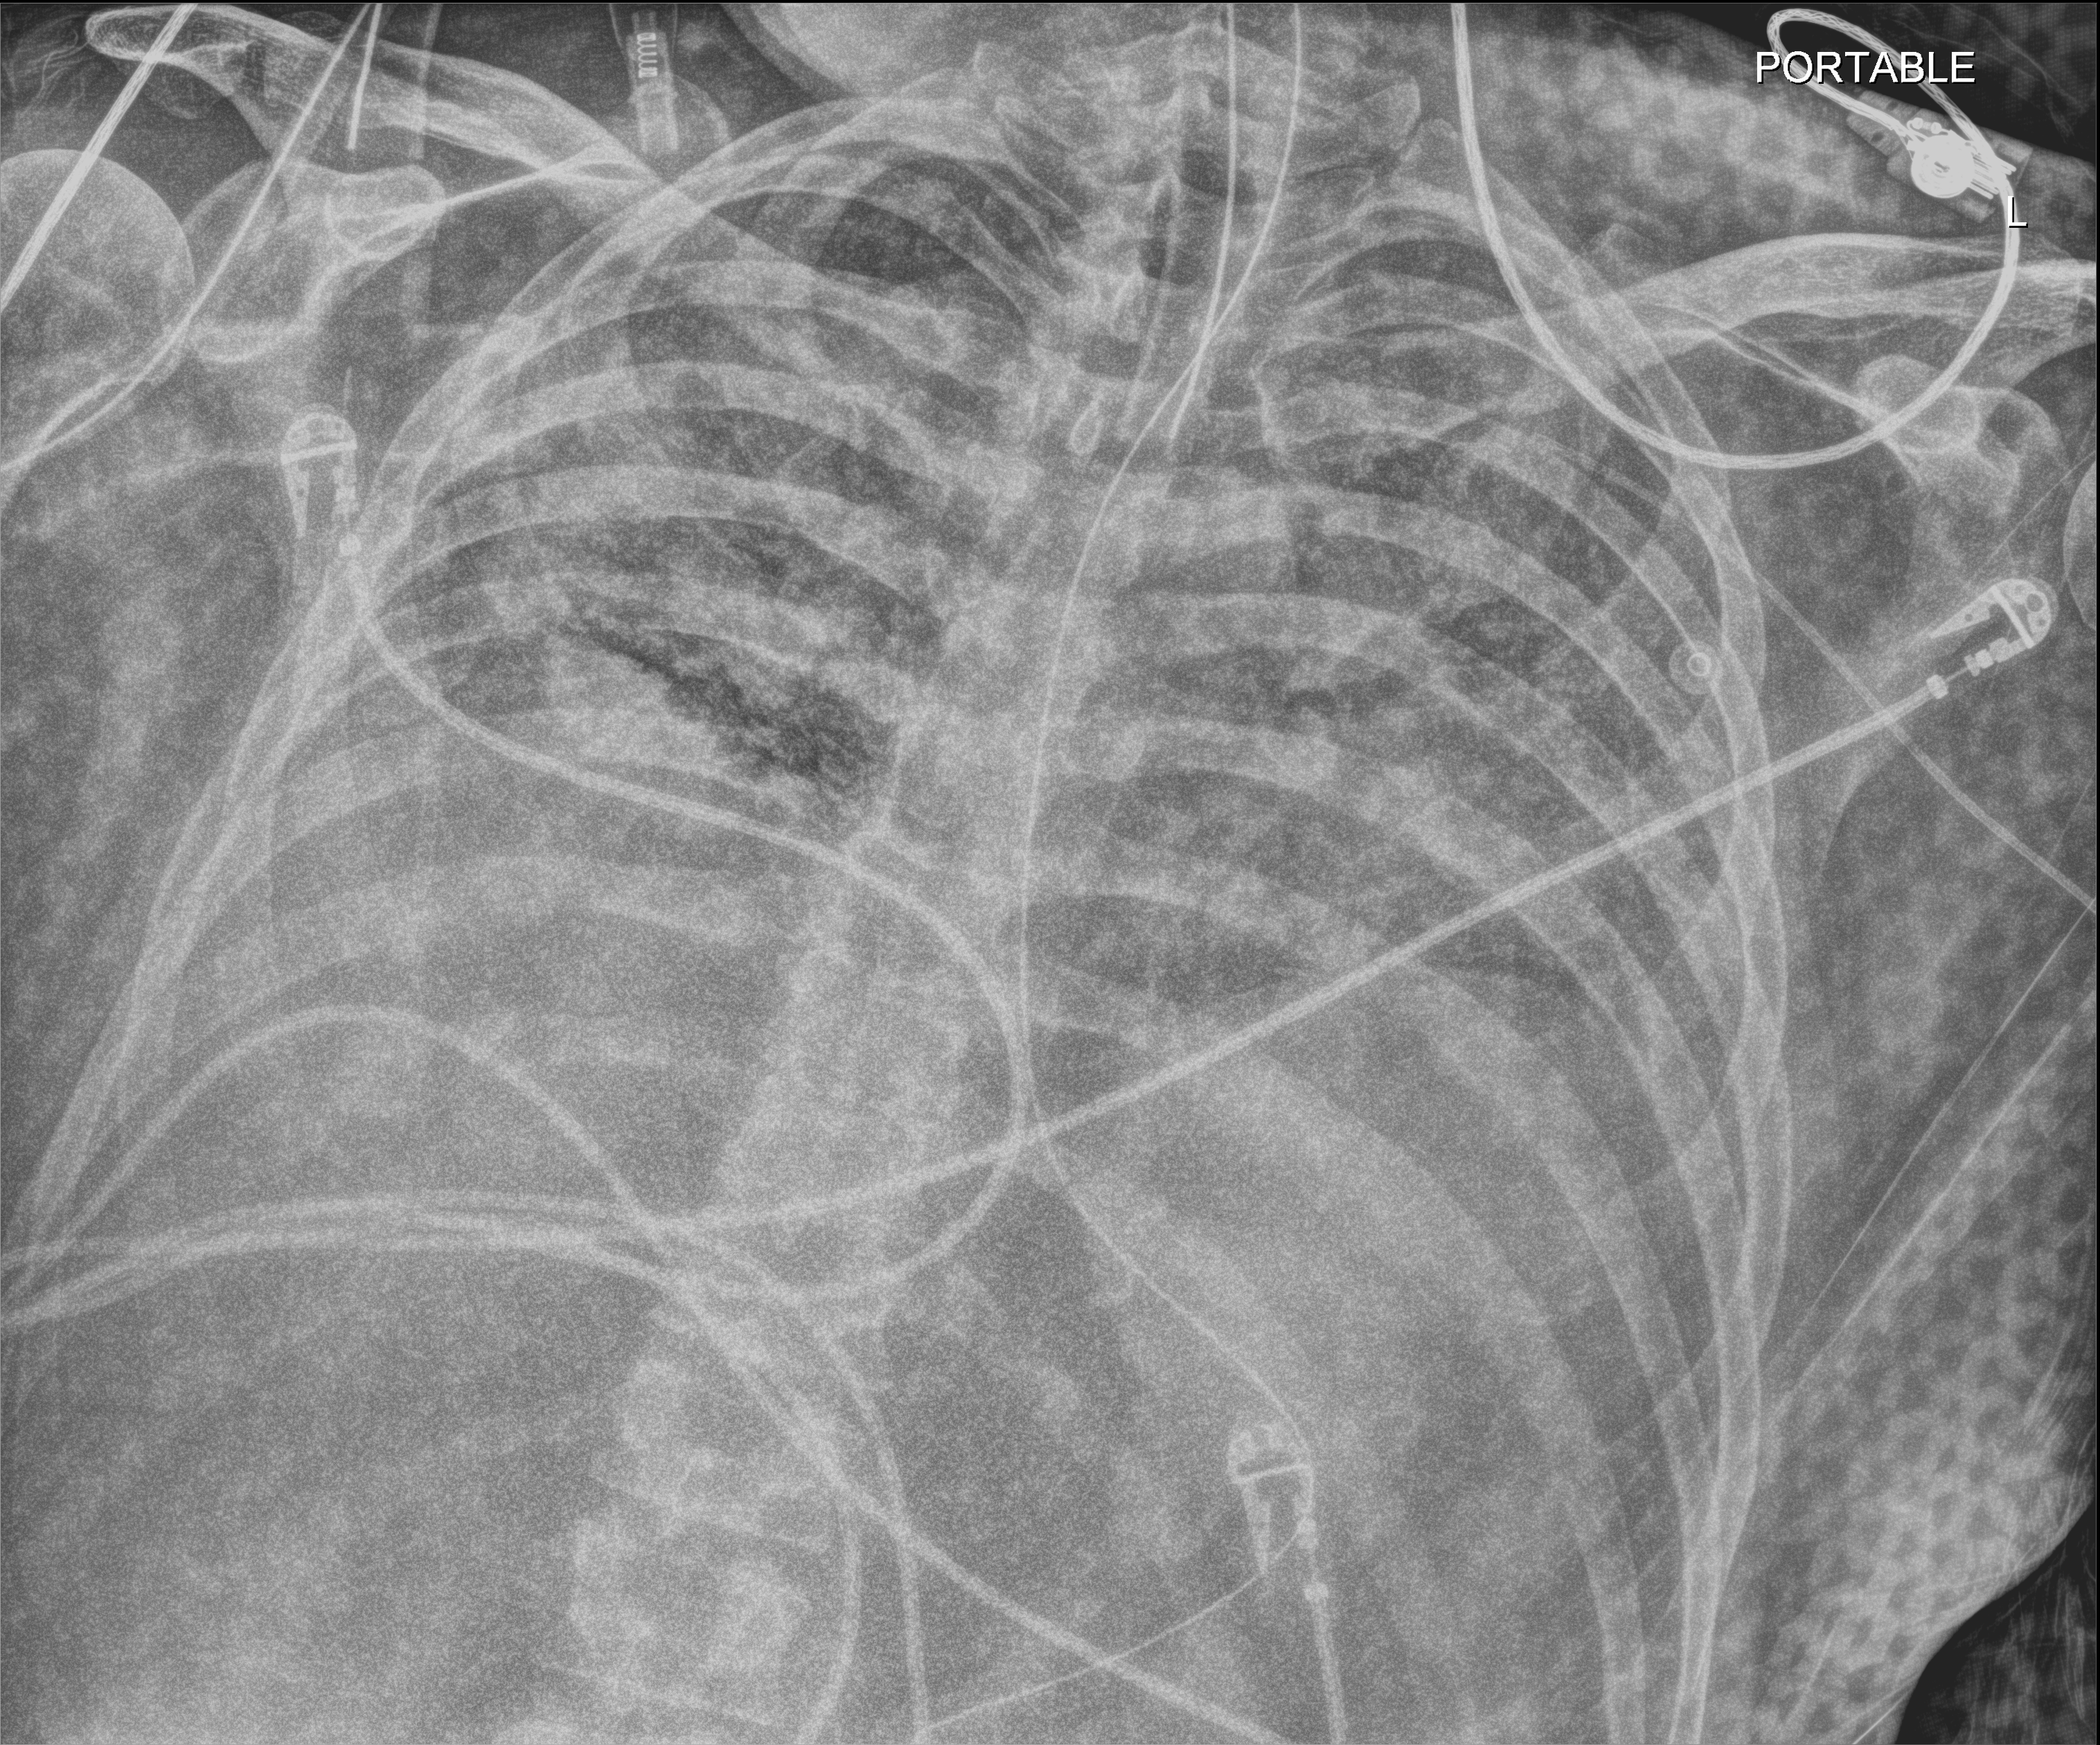
Chest X-ray (portable), anteroposterior (AP) projection. Male patient hospitalised with COVID-19, age 18–59 years.
Hospital-stay facts (about this admission, not read from this image; timing relative to this image not recorded): other chronic lung disease (admission record): no; admitted to intensive care during this hospital stay: yes.